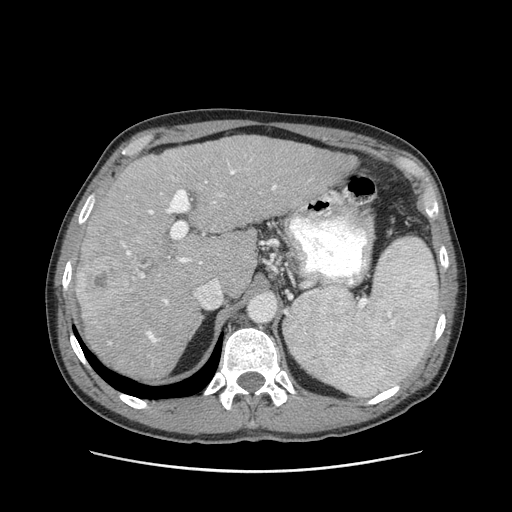
Contrast-enhanced abdominal CT (liver protocol), one axial slice; slice 65 of 93 in the series (ordered by position); 120 kVp; soft-tissue window (W 400 / L 40 HU); 2.5 mm slice thickness; 512 × 512 image matrix, field of view 380 × 380 mm. From the clinical record (not read from this slice): diagnosis: hepatocellular carcinoma (patient treated with transarterial chemoembolisation; whether this scan precedes or follows treatment is not stated here); TNM stage (as recorded): Stage-II; Child-Pugh class: A; tumour nodularity: multinodular.
Structures marked on this image (semi-automatic segmentation, software-assisted and operator-edited):
- liver parenchyma outside the tumour (the mass and vessels are separate outlines, so this box may not span the whole liver): bounding box (x1, y1, x2, y2) in pixels: (76, 136, 356, 378)
- mass: (79, 255, 132, 312)
- liver vessels: (109, 170, 277, 344)